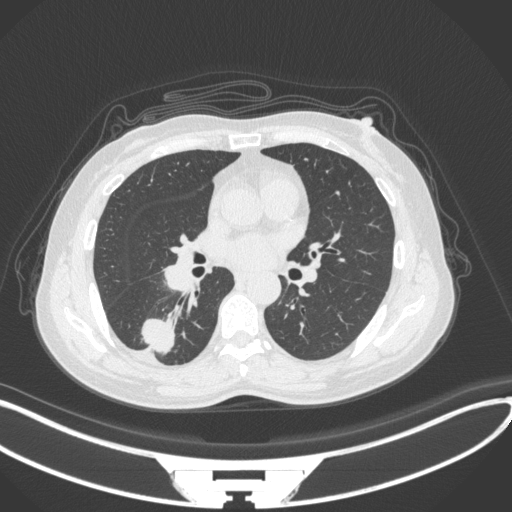
Chest CT, one axial slice; slice 155 of 352 in the series (ordered by position); 120 kVp; lung window (W 1500 / L -600 HU); 512 × 512 image matrix. Patient: female, 55 years. From the clinical record (not read from this slice): clinical TNM (as recorded): T1c N1 M0.
Outlined on this slice (rectangle marked by the reading radiologist):
- lung tumour (recorded histology: adenocarcinoma): bounding box (x1, y1, x2, y2) in pixels: (140, 314, 178, 357)